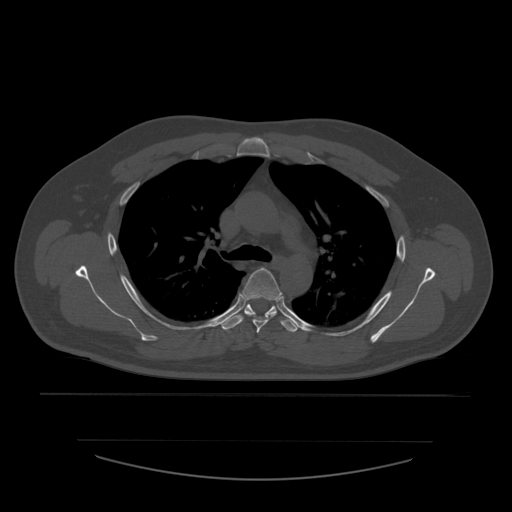
CT including the spine, one axial slice; position 409 of 532 along the scan axis; reconstruction kernel STANDARD; 120 kVp; bone window (W 1800 / L 400 HU); 512 × 512 image matrix, field of view 441 × 441 mm. Patient age 44 years. Case-level facts recorded for this patient, not image findings: primary cancer: soft tissue sarcoma.
Annotated regions visible in this slice (semi-automatically segmented with operator editing):
- T4 vertebra: box from (x=243, y=268) to (x=283, y=333) px
- T5 vertebra: (x=220, y=304)–(x=298, y=333)